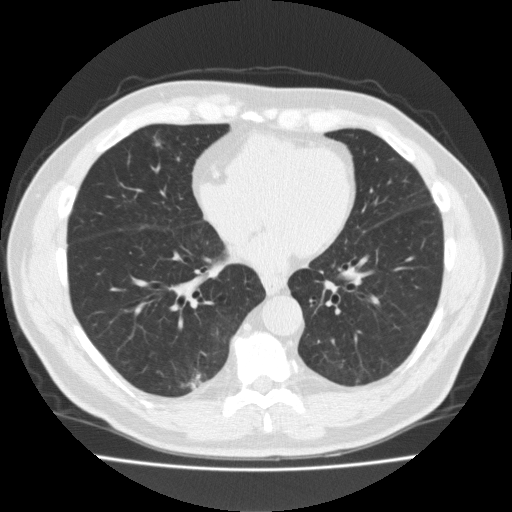
Low-dose screening chest CT, one axial slice; slice 71 of 184 in the series (ordered by position); reconstruction kernel FC10; 120 kVp; lung window (W 1500 / L -600 HU); 2 mm slice thickness; 512 × 512 image matrix, field of view 369 × 369 mm.
Outlined on this slice (outlined manually by an expert reader):
- lesion 1 (tumor, middle lobe of right lung): bounding box <156,143,160,146> (left, top, right, bottom; pixels)